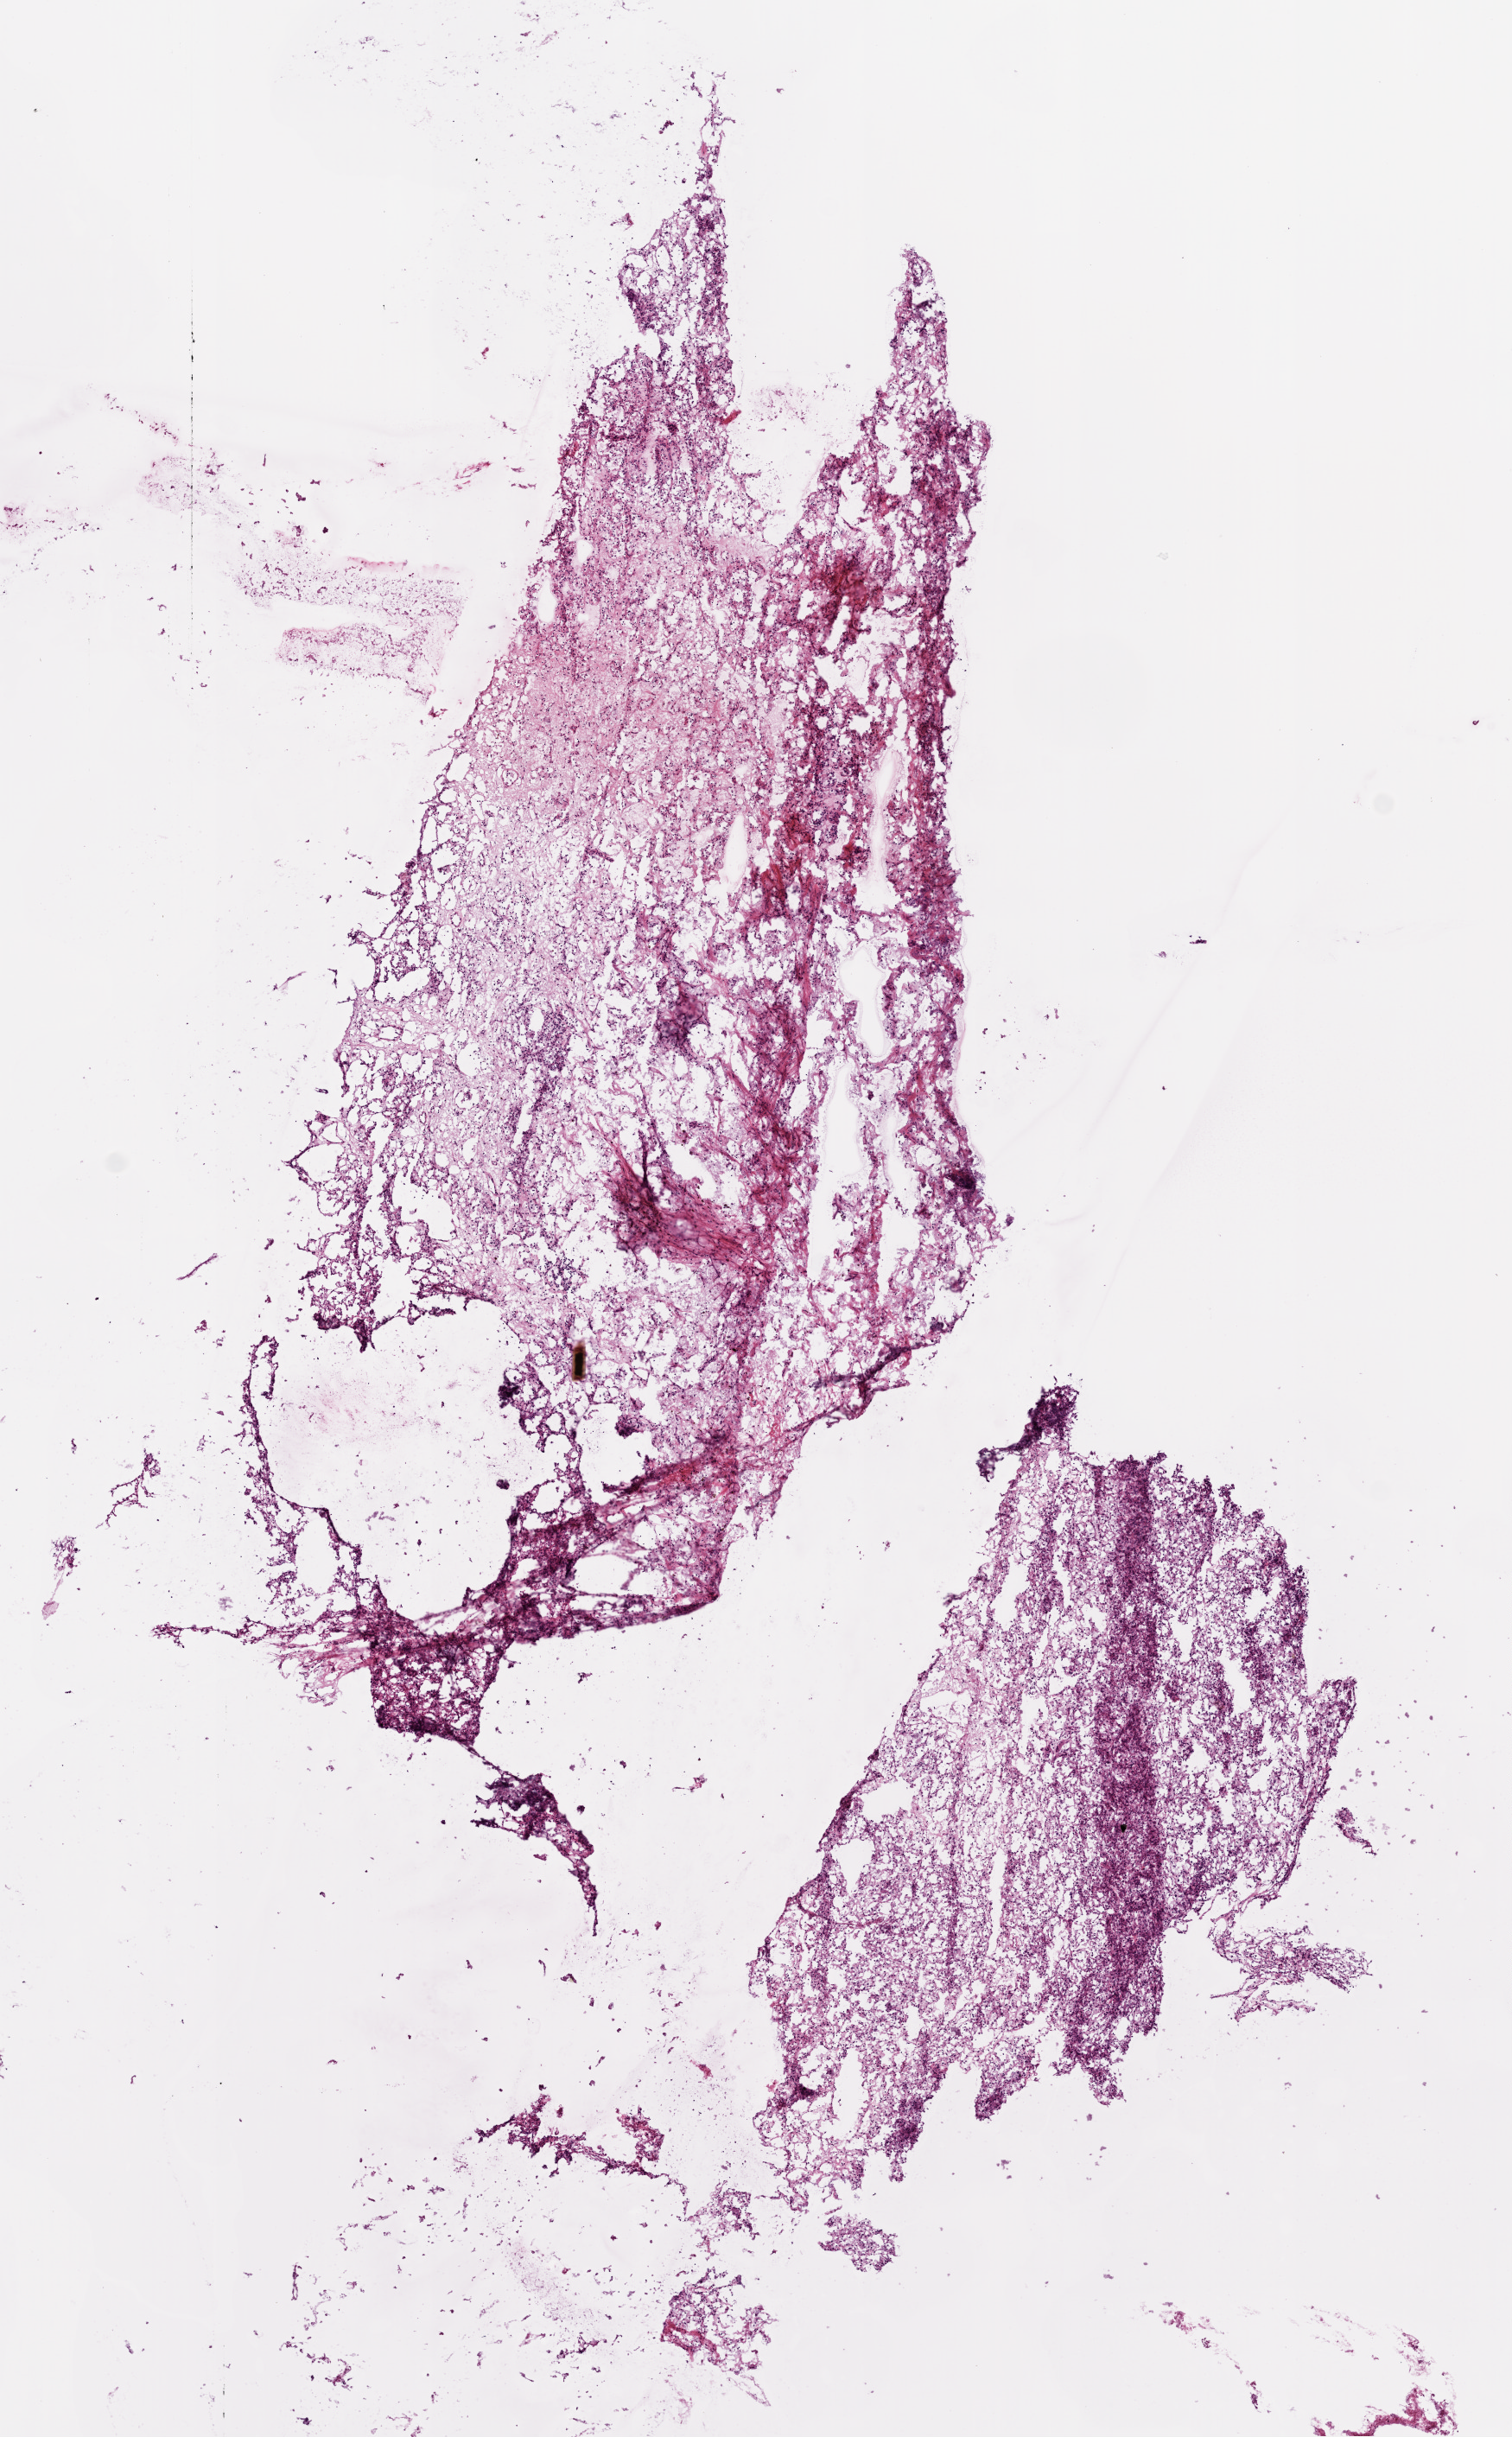
Hematoxylin and eosin (H&E) stained whole-slide image — a low-resolution overview of the entire scanned area, about 7.0 x 11.3 mm (slide scanned at 20x). Frozen section. Kidney, primary tumour sample. Patient: male, age at initial diagnosis 77 years. Histologic grade: G2 (moderately differentiated). Slide review estimates, as recorded: tumour cells 70%, tumour nuclei 75%, normal cells 0%, stromal cells 30%, necrosis 0%.
AJCC pathologic stage: I (6th edition). Diagnosis: Clear cell adenocarcinoma, NOS.